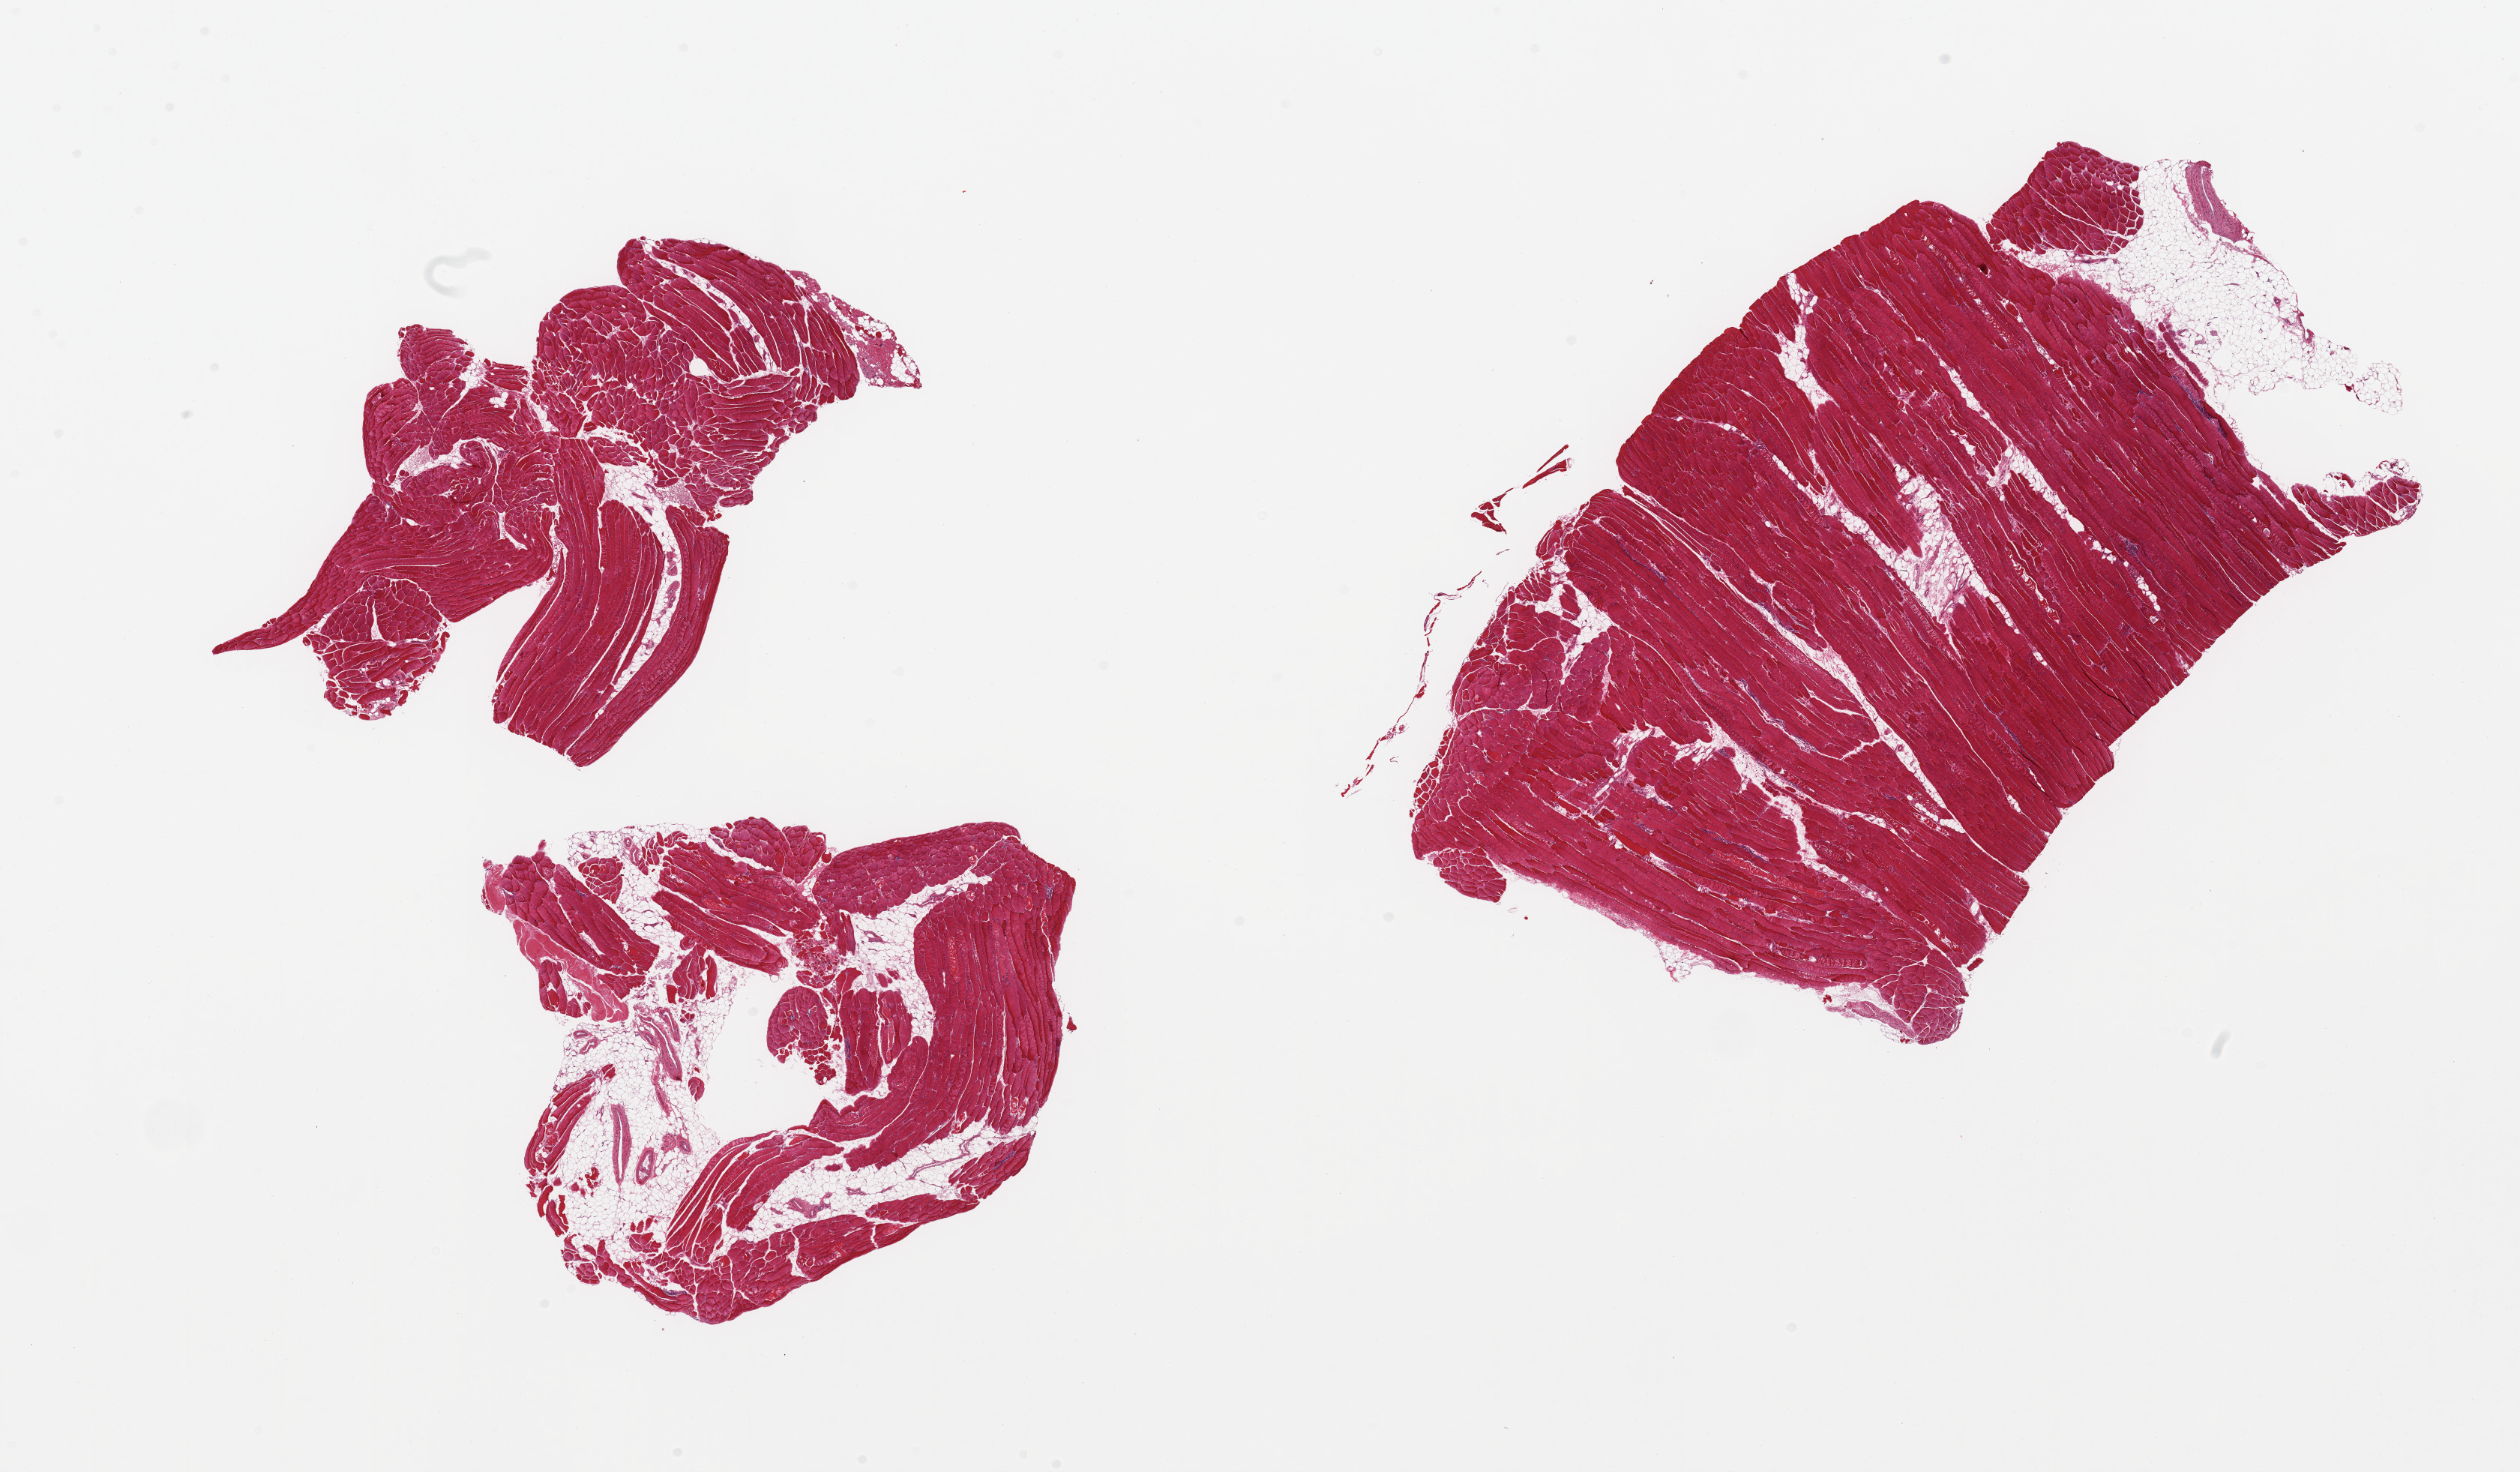
Haematoxylin and eosin whole-slide image, brightfield, shown as a low-resolution overview of the whole scanned area (about 26.6 x 15.5 mm); PAXgene-fixed, paraffin-embedded tissue; section of skeletal muscle (target tissue); tissue donor sample.
Pathologist's review note for this sample: 3 pieces, adherent interstitial fat is ~10% tissue.